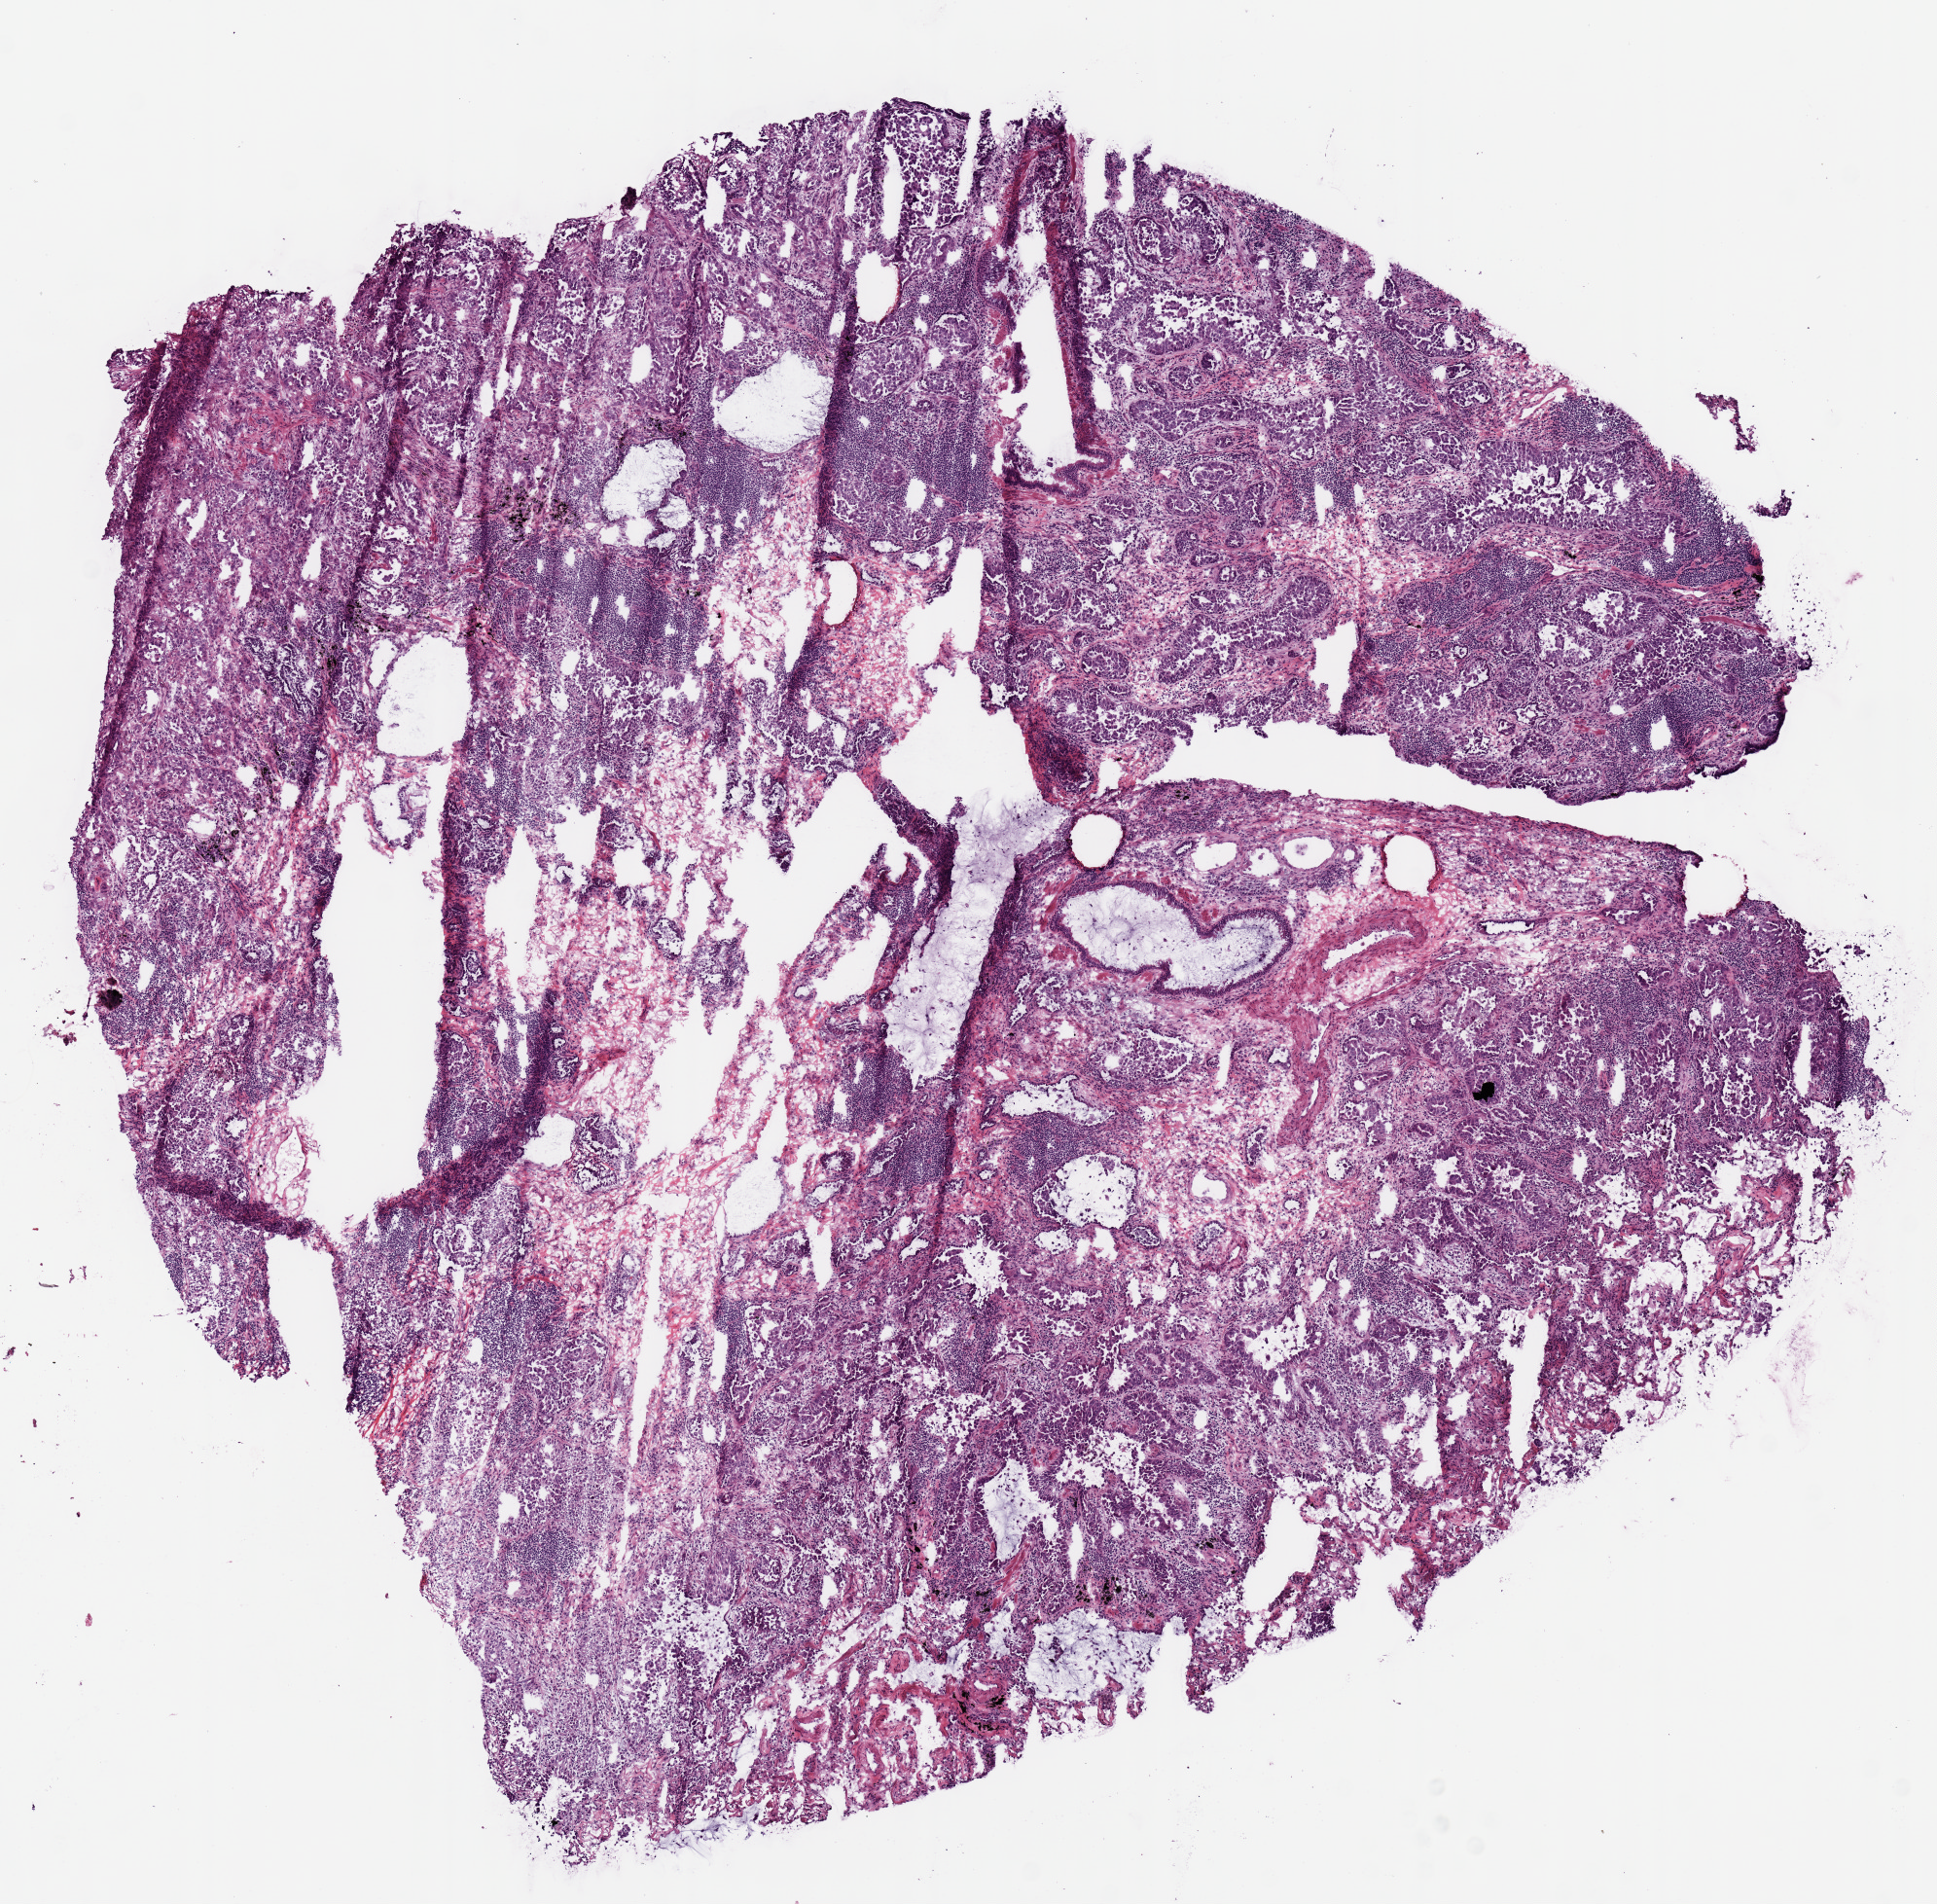
H&E-stained whole-slide image — a low-resolution overview of the entire scanned area, about 7.9 x 7.7 mm (acquisition: 20x scan); frozen section; lung, primary tumour sample. Female patient; age at initial diagnosis 63 years. Composition of this section per pathologist review: tumour cells 80%, tumour nuclei 70%, normal cells 0%, stromal cells 20%, necrosis 0%. Infiltration values recorded for this section: lymphocyte infiltration 0%, monocyte infiltration 0%, neutrophil infiltration 0%.
AJCC pathologic stage: IIA (7th edition). Pathologic diagnosis: Adenocarcinoma, NOS (lower lobe, lung). TNM: T1b N1 M0.